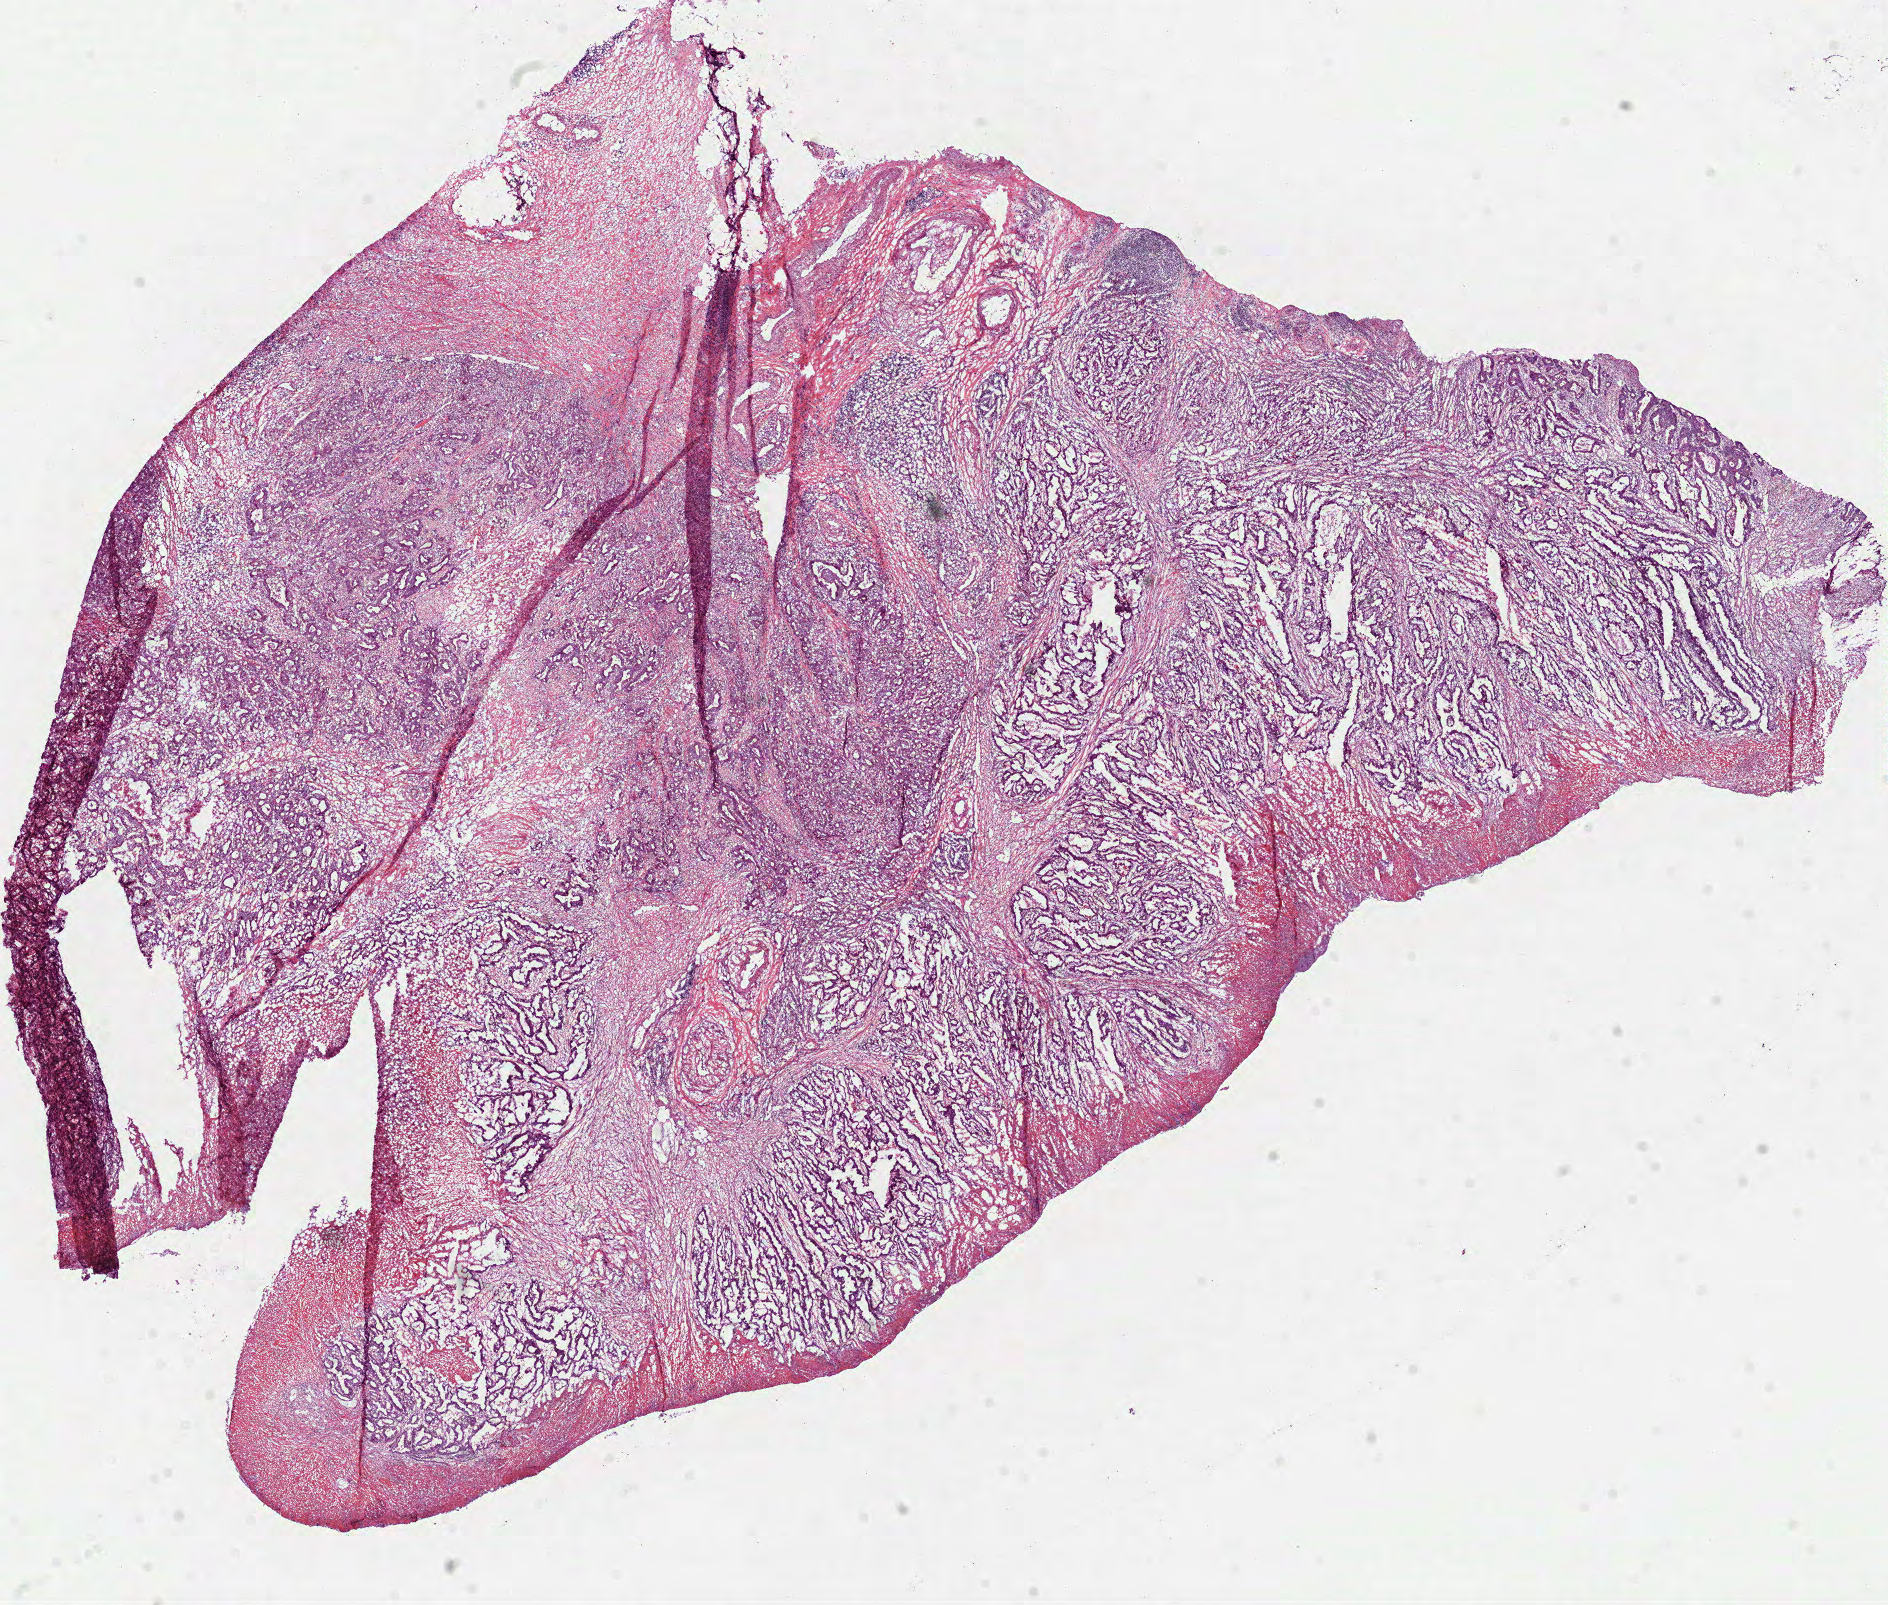
Whole-slide histology image, H&E — shown as a low-resolution overview of the whole scanned area (about 15.2 x 12.9 mm, slide scanned at 40x). Frozen section from the top of the tissue portion. Colon, primary tumour sample. Male patient; age at initial diagnosis 68 years. Pathologist review of this section (percent, as recorded): tumour cells 75%, tumour nuclei 80%, normal cells 0%, stromal cells 20%, necrosis 5%.
Diagnosis: Adenocarcinoma, NOS (sigmoid colon). AJCC pathologic stage: II (5th edition).